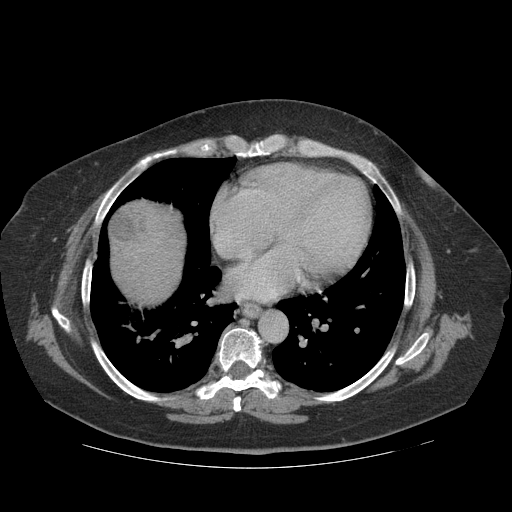
Contrast-enhanced abdominal CT (liver protocol), one axial slice. Slice 110 of 121 in the series (ordered by position). Reconstruction kernel STANDARD. 140 kVp. Soft-tissue window (W 400 / L 40 HU). 512 × 512 image matrix, field of view 420 × 420 mm. Case-level facts recorded for this patient, not image findings: diagnosis: hepatocellular carcinoma (patient treated with transarterial chemoembolisation; whether this scan precedes or follows treatment is not stated here); TNM stage (as recorded): Stage-IIIA; Child-Pugh class: A; tumour differentiation: well differentiated; tumour nodularity: multinodular.
Outlined on this slice (semi-automatically segmented with operator editing):
- liver parenchyma outside the tumour (the mass and vessels are separate outlines, so this box may not span the whole liver): bounding box (x1, y1, x2, y2) in pixels: (108, 198, 184, 304)
- mass: (109, 205, 143, 244)